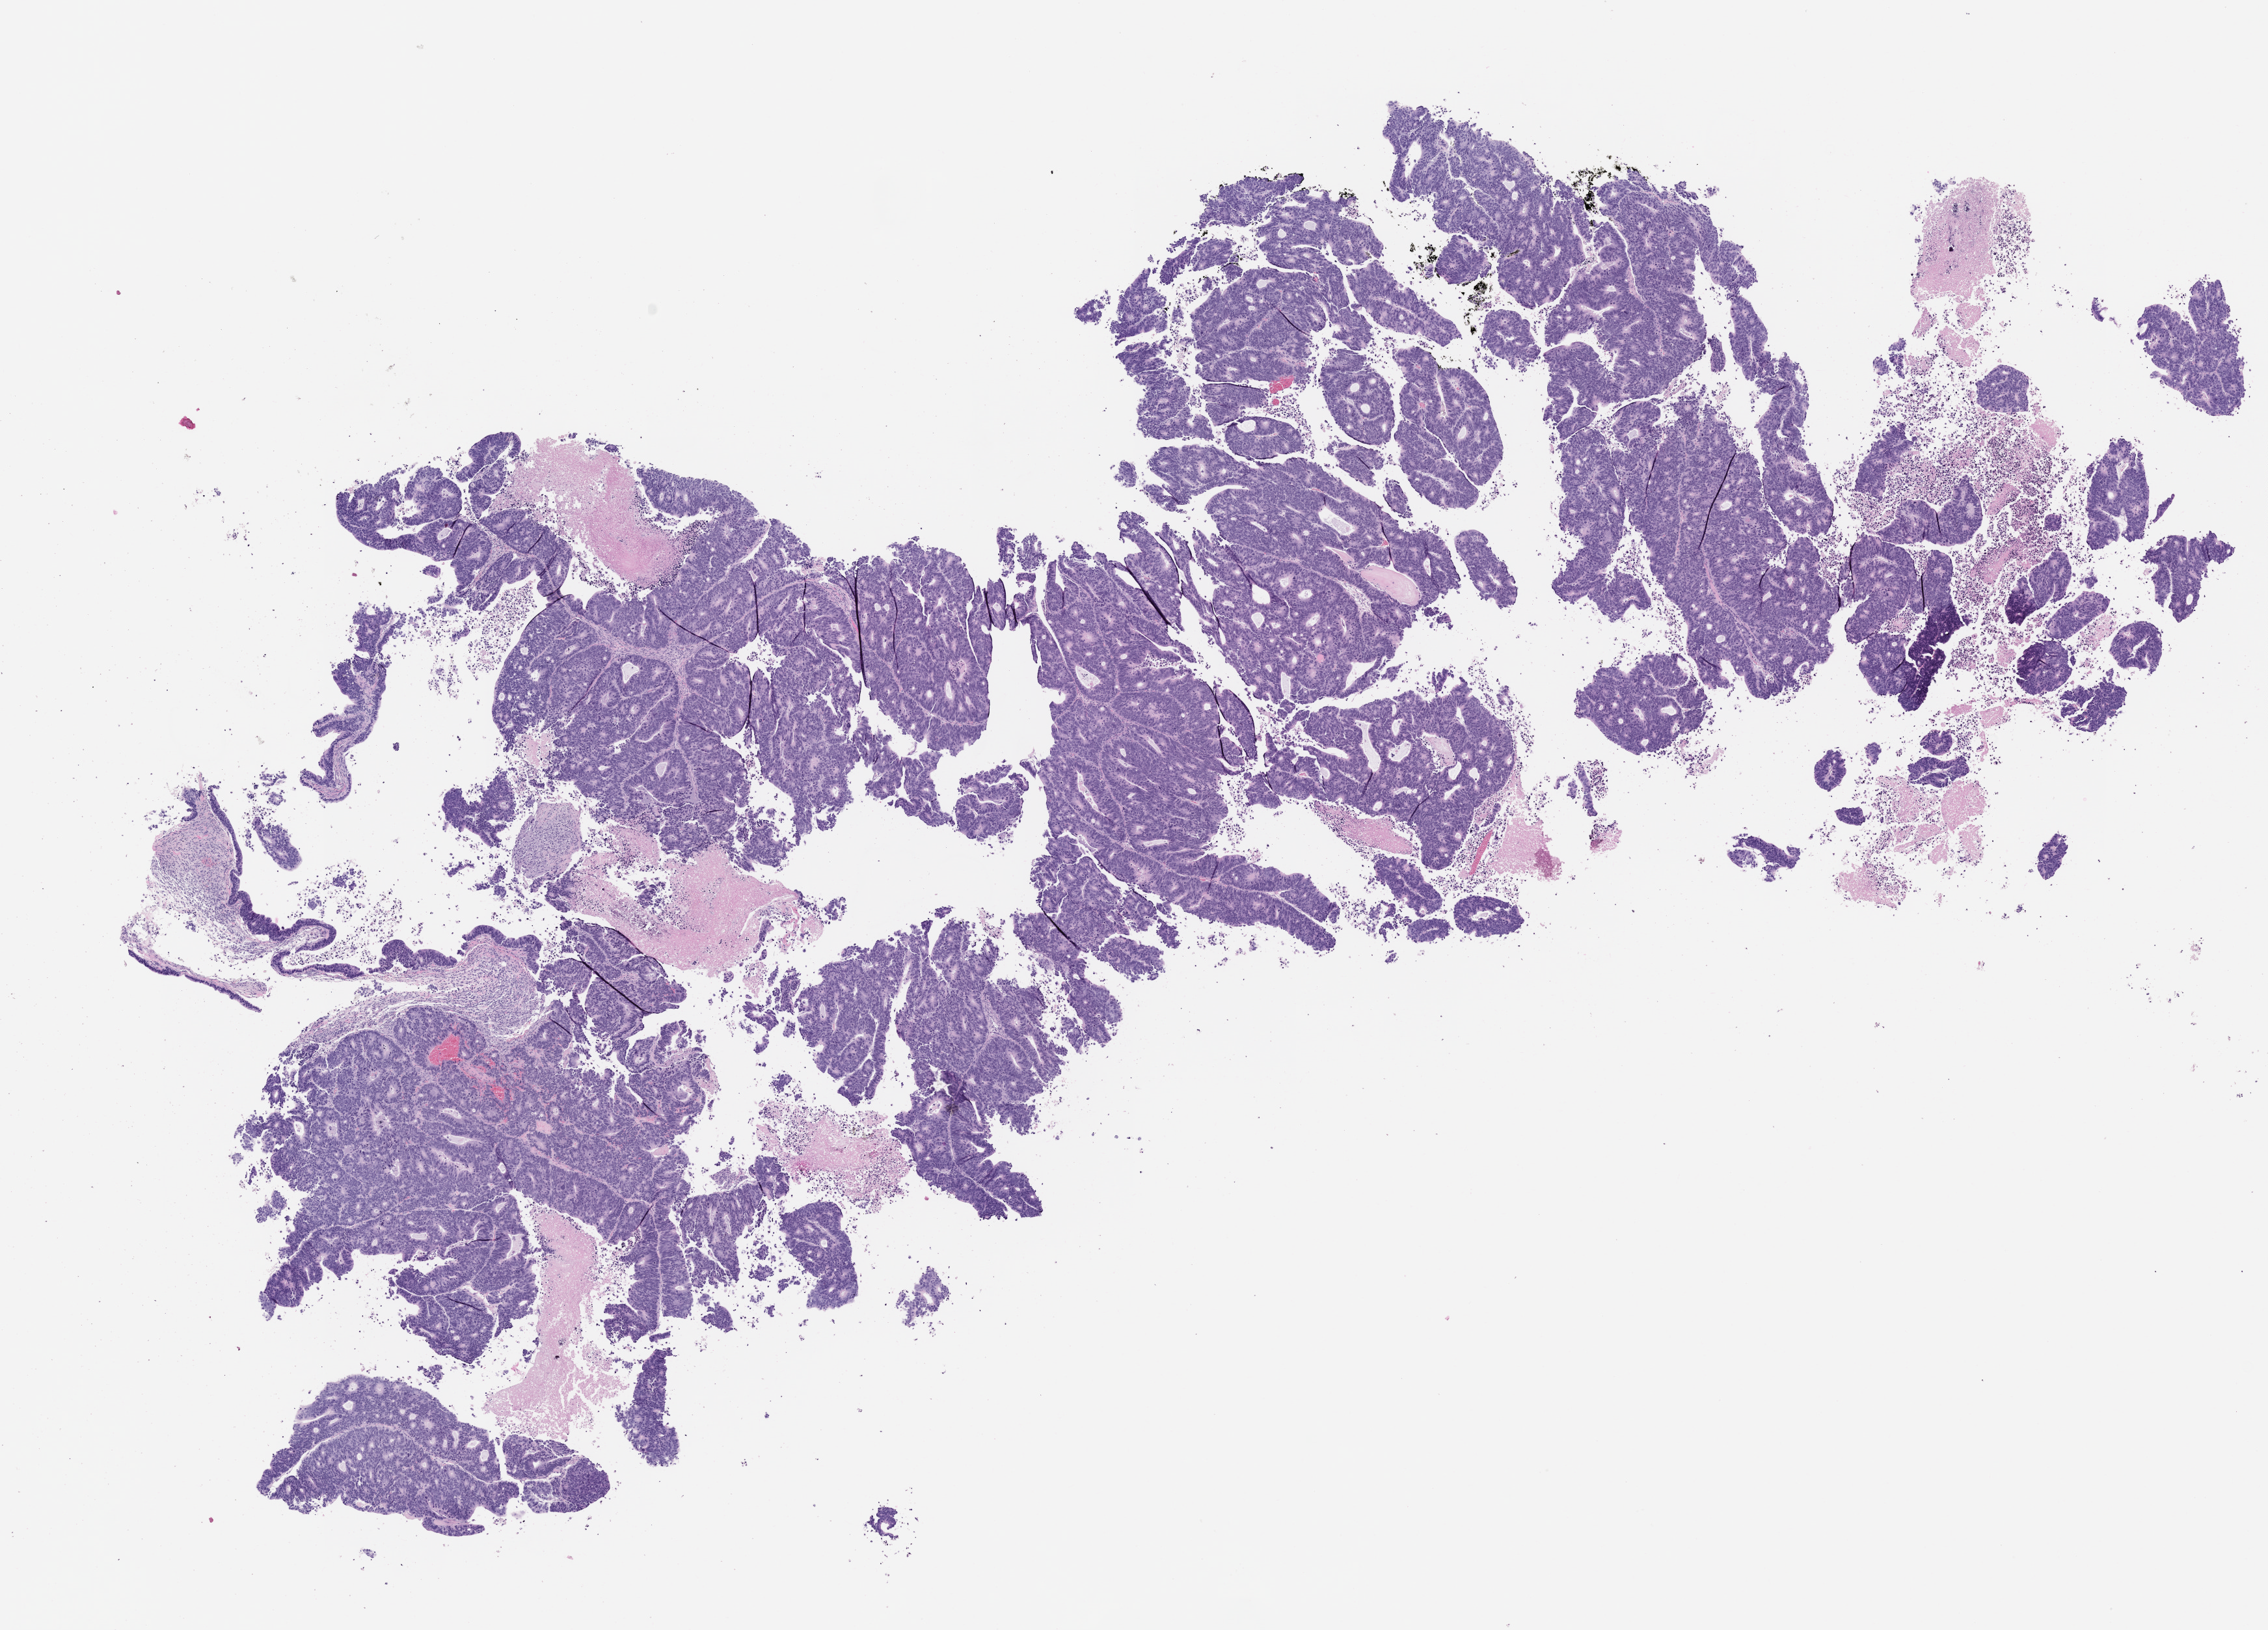
H&E whole-slide image of a patient-derived xenograft (PDX) tumor grown in a mouse, passage 3 — a low-resolution overview of the entire scanned area, about 14.0 x 10.1 mm. FFPE section. Tumor site category: colon.
Originating patient diagnosis: Colon Adenocarcinoma.